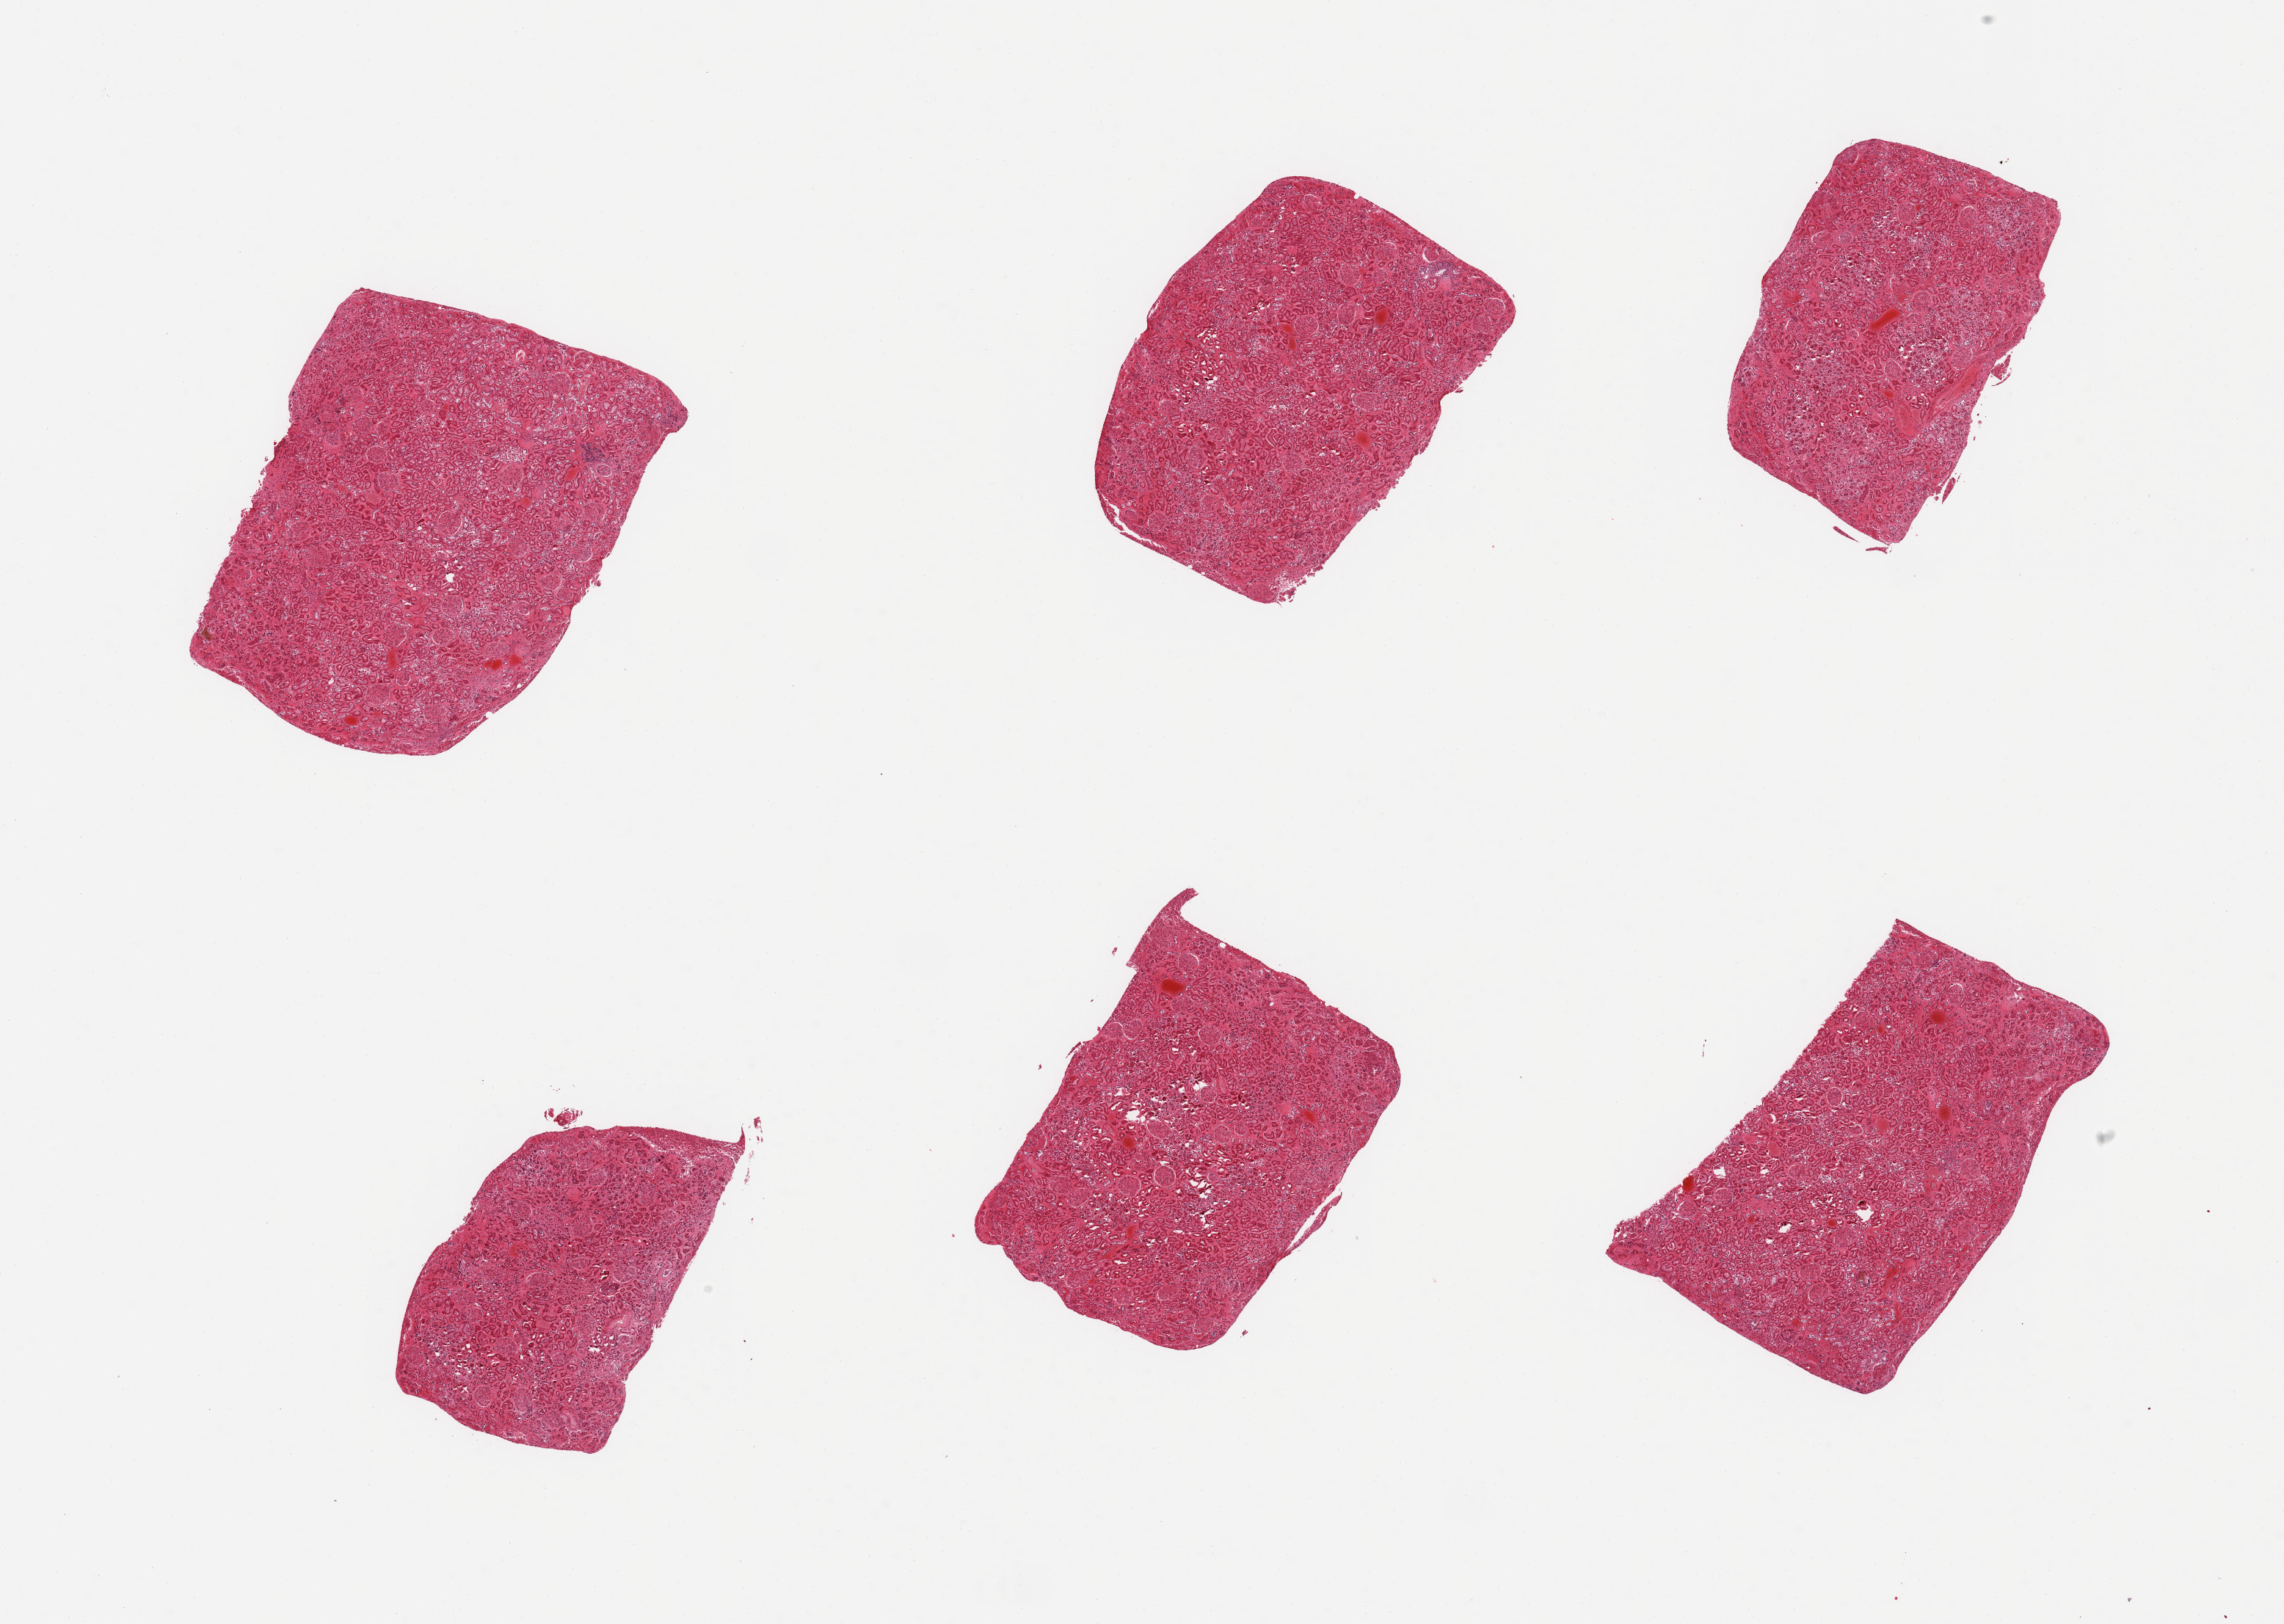
Whole-slide image, hematoxylin and eosin (H&E) stain, a low-resolution overview of the entire scanned area, about 24.6 x 17.5 mm. PAXgene-fixed paraffin-embedded (PFPE) section. Sampled site (target tissue): renal cortex. Donor tissue sample. Donor sex: male.
* pathologist's review note for this sample: 6 pieces, glomeruli present; advanced autolysis